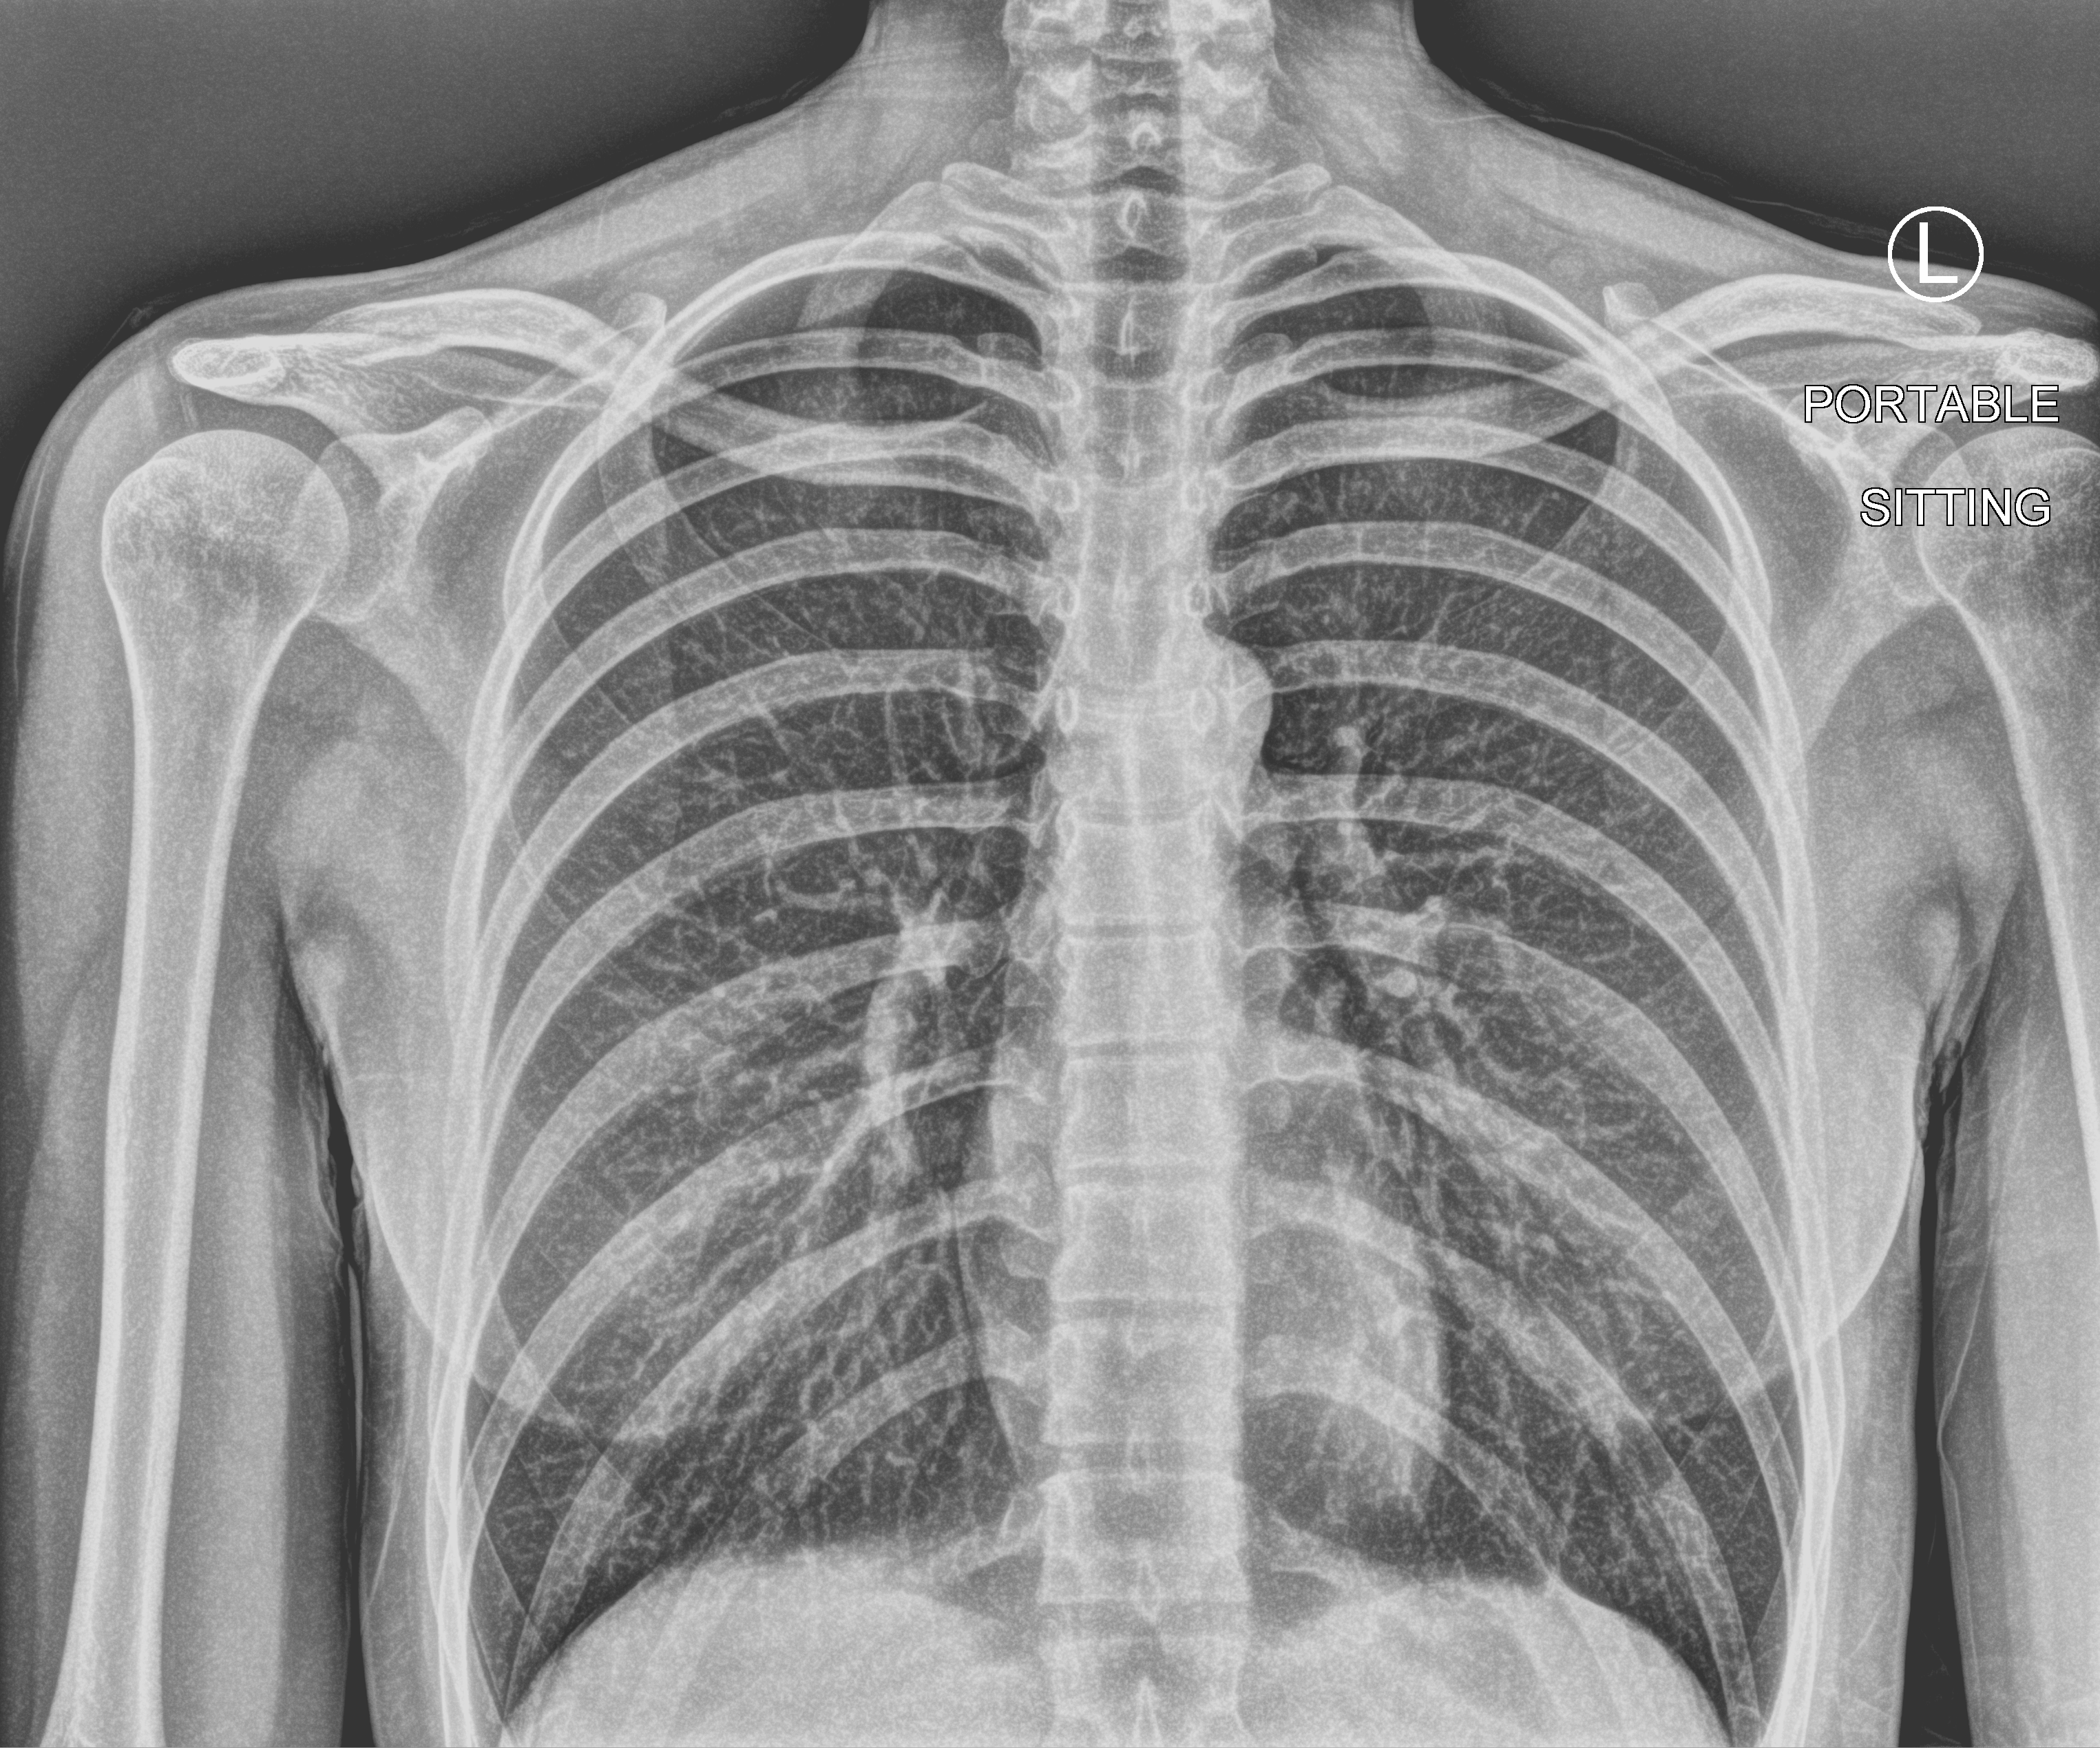
Chest X-ray (portable), anteroposterior (AP) projection. Patient hospitalised with COVID-19; female, aged 18–59 years.
From the hospital-stay record, not from the radiograph (when in the stay this image was taken is not recorded): mechanically ventilated during this hospital stay: no; admitted to intensive care during this hospital stay: no.